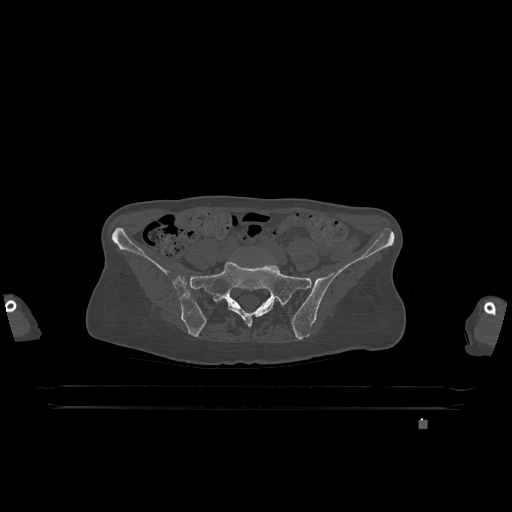
CT including the spine, one axial slice; position 194 of 1317 along the scan axis; bone window (W 1800 / L 400 HU); 0.5 mm slice thickness; 512 × 512 image matrix, field of view 500 × 500 mm. Patient: female, 74 years. From the clinical record (not read from this slice): primary cancer: lung; vertebrae with lytic lesions (as recorded): T1, T4, T5, T6, L4, L5.
Structures marked on this image (semi-automatically segmented with operator editing):
- L5 vertebra: bounding box <276,299,278,301> (left, top, right, bottom; pixels)